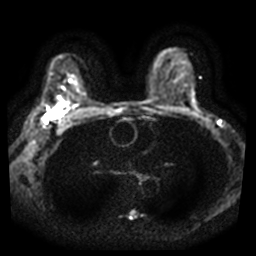
Breast MRI, one axial slice; position 23 of 37 along the scan axis; diffusion-weighted series; image 2 of 4 stored at this slice position (different b-values; order by instance number); 3 T; 256 × 256 image matrix. Female patient.
Structures marked on this image (manually delineated by an expert):
- tumour on diffusion-weighted imaging: bounding box <46,108,62,123> (left, top, right, bottom; pixels)